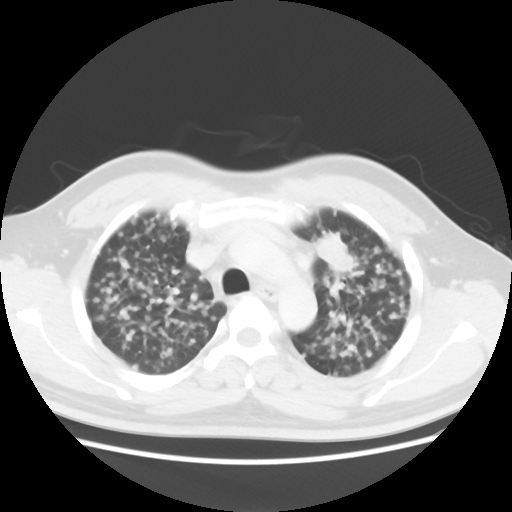
Chest CT, one axial slice; slice 29 of 40 in the series (ordered by position); reconstruction kernel STANDARD; 120 kVp; lung window (W 1500 / L -600 HU); 5 mm slice thickness; 512 × 512 image matrix, field of view 366 × 366 mm. Patient: male, 41 years. Case-level facts recorded for this patient, not image findings: clinical TNM (as recorded): T1c N3 M1b; histopathological grade: G2-3.
Structures marked on this image (rectangle marked by the reading radiologist):
- lung tumour (recorded histology: adenocarcinoma): bounding box [x1, y1, x2, y2] px = [310, 228, 357, 271]